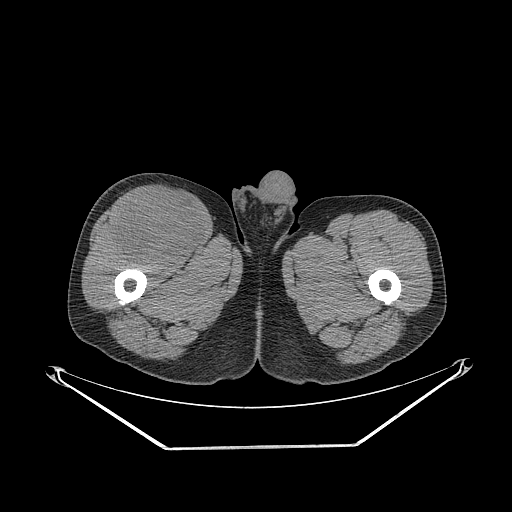
CT of an extremity soft-tissue mass (from a PET/CT study), one axial slice; slice 289 of 311 in the series (ordered by position); 140 kVp; soft-tissue window (W 400 / L 40 HU); 3.75 mm slice thickness; 512 × 512 image matrix, field of view 500 × 500 mm. Male patient. From the clinical record (not read from this slice): histological type: pleiomorphic leiomyosarcoma; grade: intermediate; site of the primary tumour: right thigh.
Annotated regions visible in this slice (expert contour drawn on MRI and transferred to this co-registered scan by the dataset authors):
- gross tumour volume including surrounding oedema: bounding box (x1, y1, x2, y2) in pixels: (114, 190, 204, 264)
- gross tumour volume (mass): (116, 190, 204, 264)